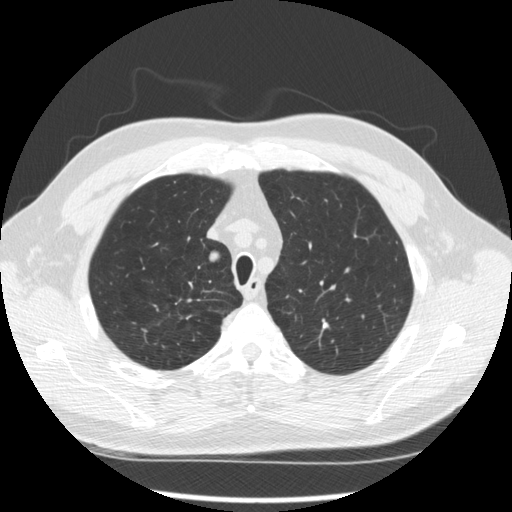
Low-dose screening chest CT, axial slice, second screening round (one year after baseline), lung window (W 1500 / L -600 HU), standard (soft-tissue) reconstruction kernel (STANDARD), 120 kVp. Male, age 64 years at enrolment. Former smoker at enrolment.
- Expert reader's lesion annotation, box from (x=194, y=245) to (x=226, y=274) px.
- The screening reader recorded 3 non-calcified nodules or masses ≥4 mm on this exam; which of them this box marks is not recorded.